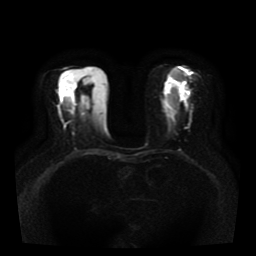
Breast MRI, one axial slice; position 21 of 41 along the scan axis; diffusion-weighted series; image 2 of 4 stored at this slice position (different b-values; order by instance number); 1.5 T; 256 × 256 image matrix. Female patient.
Annotated regions visible in this slice (outlined manually by an expert reader):
- tumour on diffusion-weighted imaging: bounding box [x1, y1, x2, y2] px = [188, 92, 191, 94]